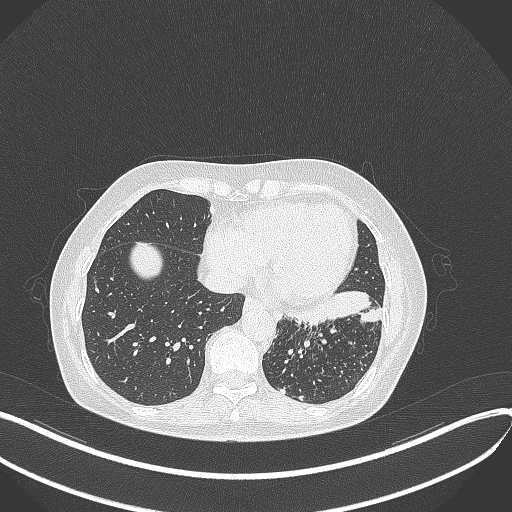
Chest CT, one axial slice; position 126 of 429 along the scan axis; 100 kVp; lung window (W 1500 / L -600 HU); 512 × 512 image matrix, field of view 400 × 400 mm. Female patient, age 63 years. Case-level facts recorded for this patient, not image findings: clinical TNM (as recorded): T1b N0 M0; histopathological grade: G2-3.
Structures marked on this image (rectangle marked by the reading radiologist):
- lung tumour (recorded histology: adenocarcinoma): box from (x=286, y=289) to (x=379, y=334) px